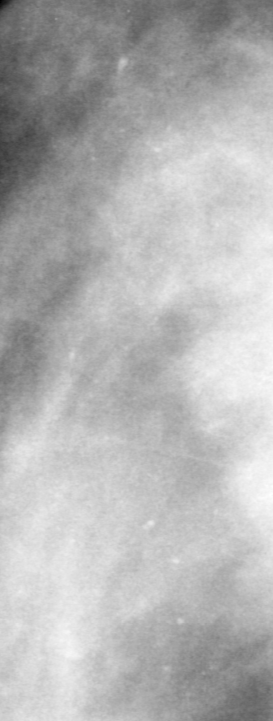
Cropped region of a digitized screen-film mammogram centred on a radiologist-marked abnormality, left breast, MLO view.
- Calcifications, morphology punctate, distribution segmental; BI-RADS assessment category 4; subtlety rating 2 on a 1 (subtle) to 5 (obvious) scale; pathology (as recorded): malignant.